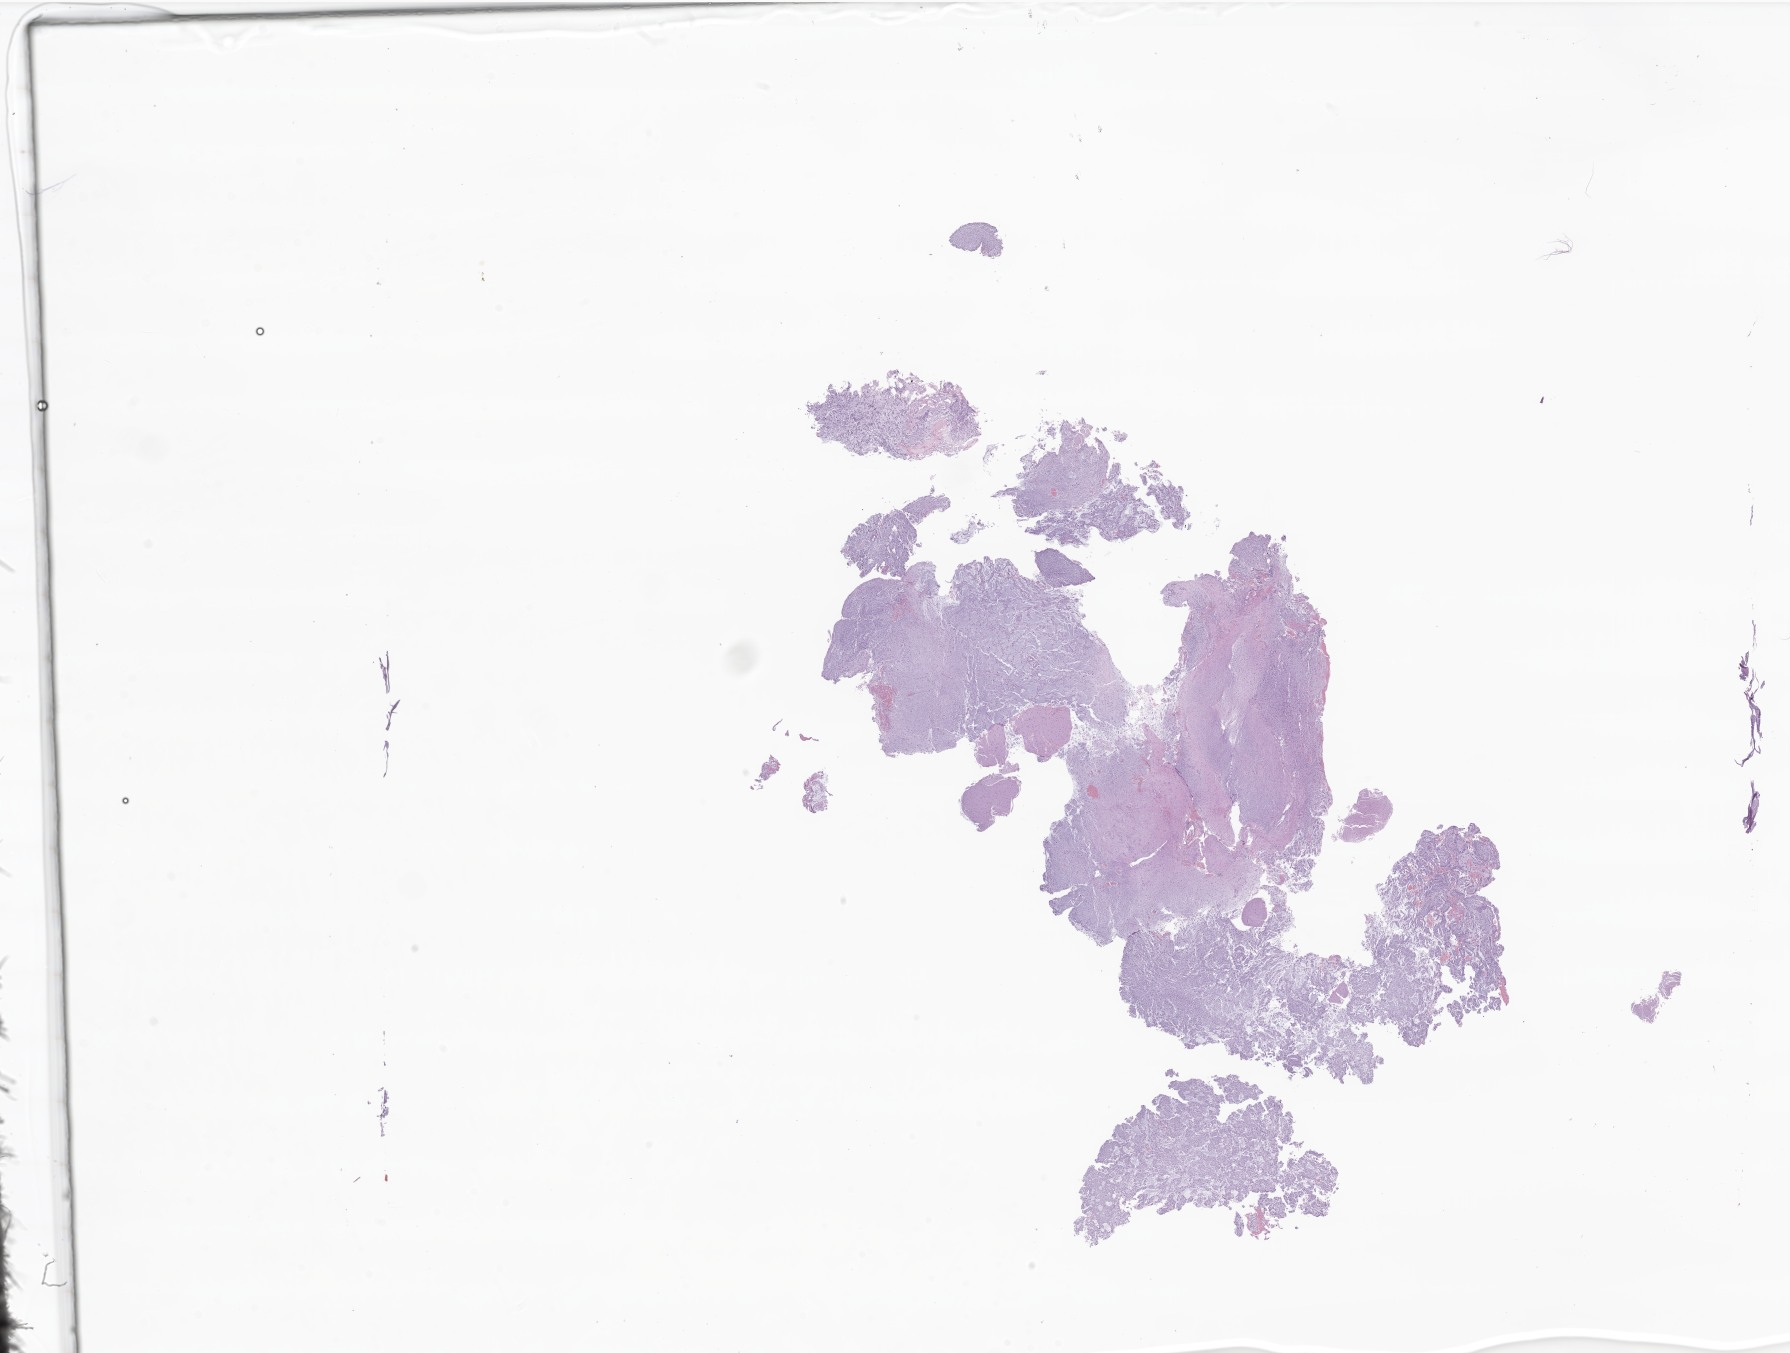
Whole-slide image, haematoxylin and eosin stain of tumor tissue from the brain — a low-resolution overview of the entire scanned area, about 30.2 x 22.8 mm. FFPE section. Patient female; age 204 months (17 years).
Diagnosis: Neoplasm, uncertain whether benign or malignant.